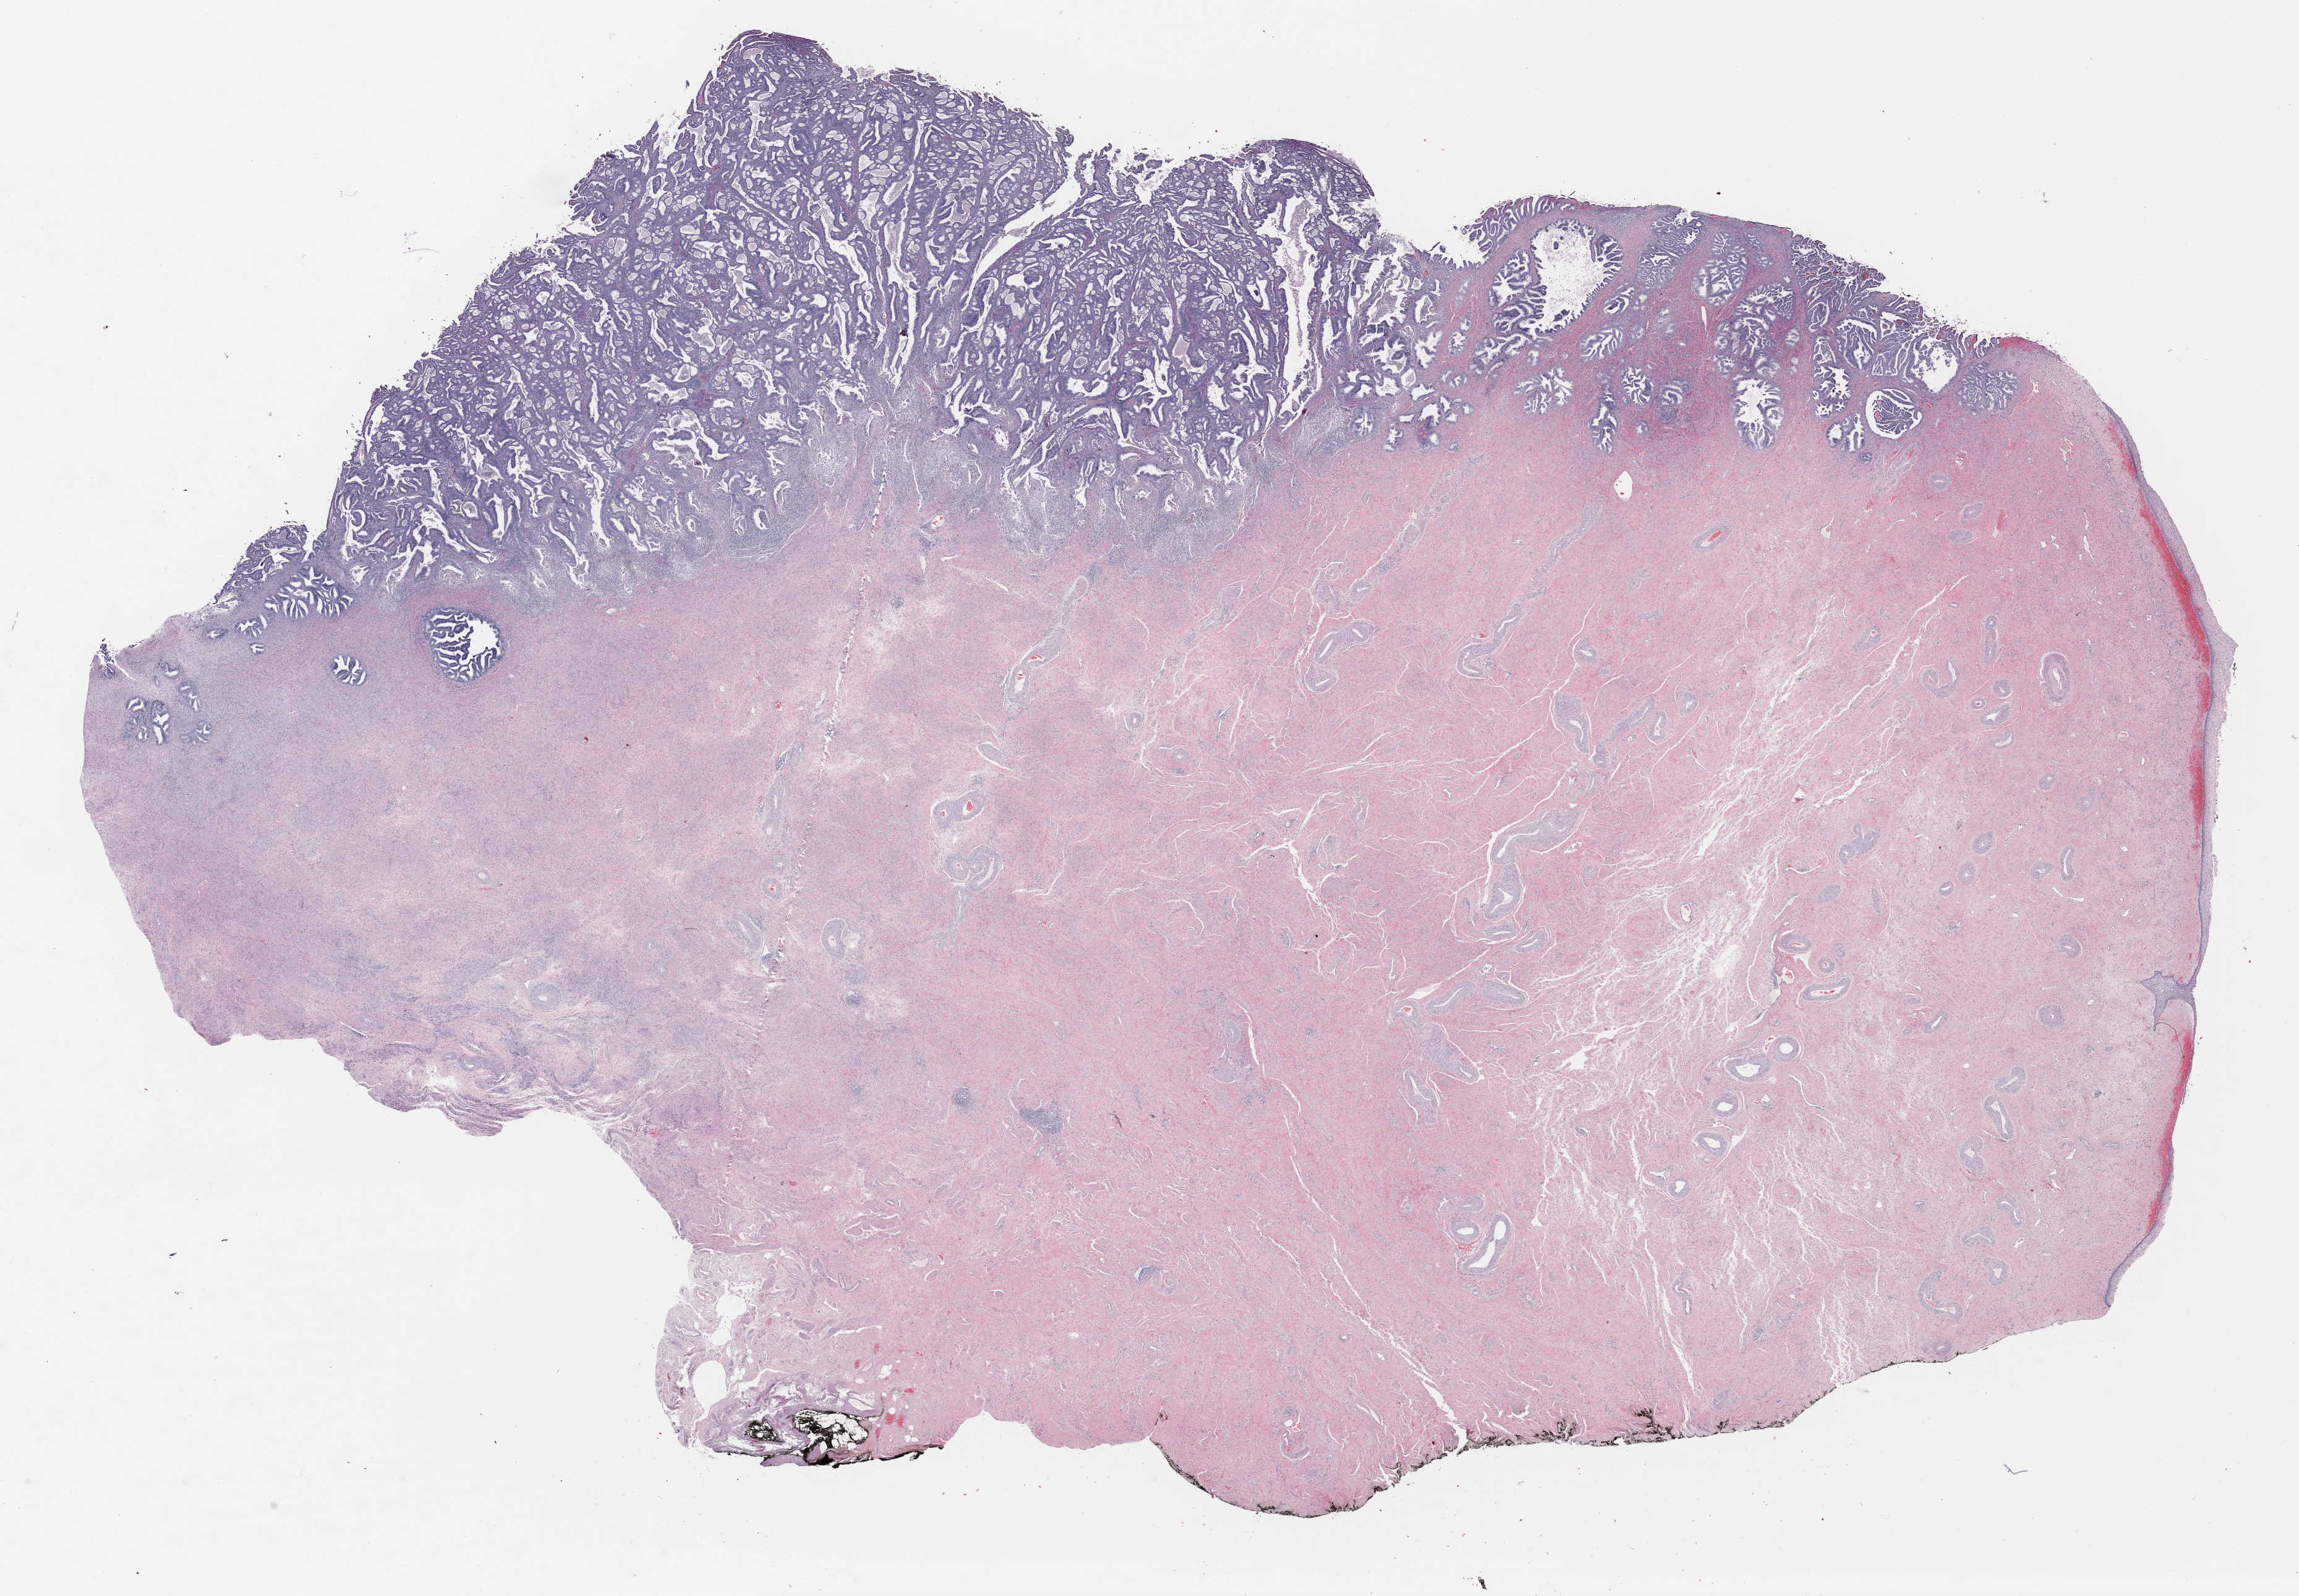
Whole-slide histology image, H&E-stained — whole scanned area (about 29.2 x 20.3 mm, slide scanned at 40x) shown as a low-resolution overview; formalin-fixed paraffin-embedded (FFPE) diagnostic section; sample: primary tumour, cervix. Patient: female, age at initial diagnosis 64 years. Histologic grade: G2 (moderately differentiated).
- FIGO stage: IB1
- pathologic diagnosis: Adenocarcinoma, endocervical type (cervix uteri)
- lymph nodes positive (case pathology): 0 of 16 examined